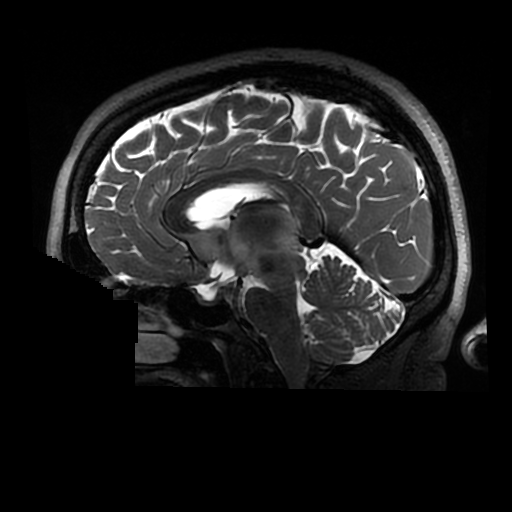
Brain MRI from a brain-tumour surgery series, one sagittal slice. Position 153 of 320 along the scan axis. 0.6 mm slice thickness. 512 × 512 image matrix, field of view 240 × 240 mm. Case-level facts recorded for this patient, not image findings: histopathology: Astrocytoma; WHO grade: 2; IDH mutation: yes.
Outlined on this slice (outlined manually by an expert reader):
- tumour: box from (x=276, y=209) to (x=295, y=254) px